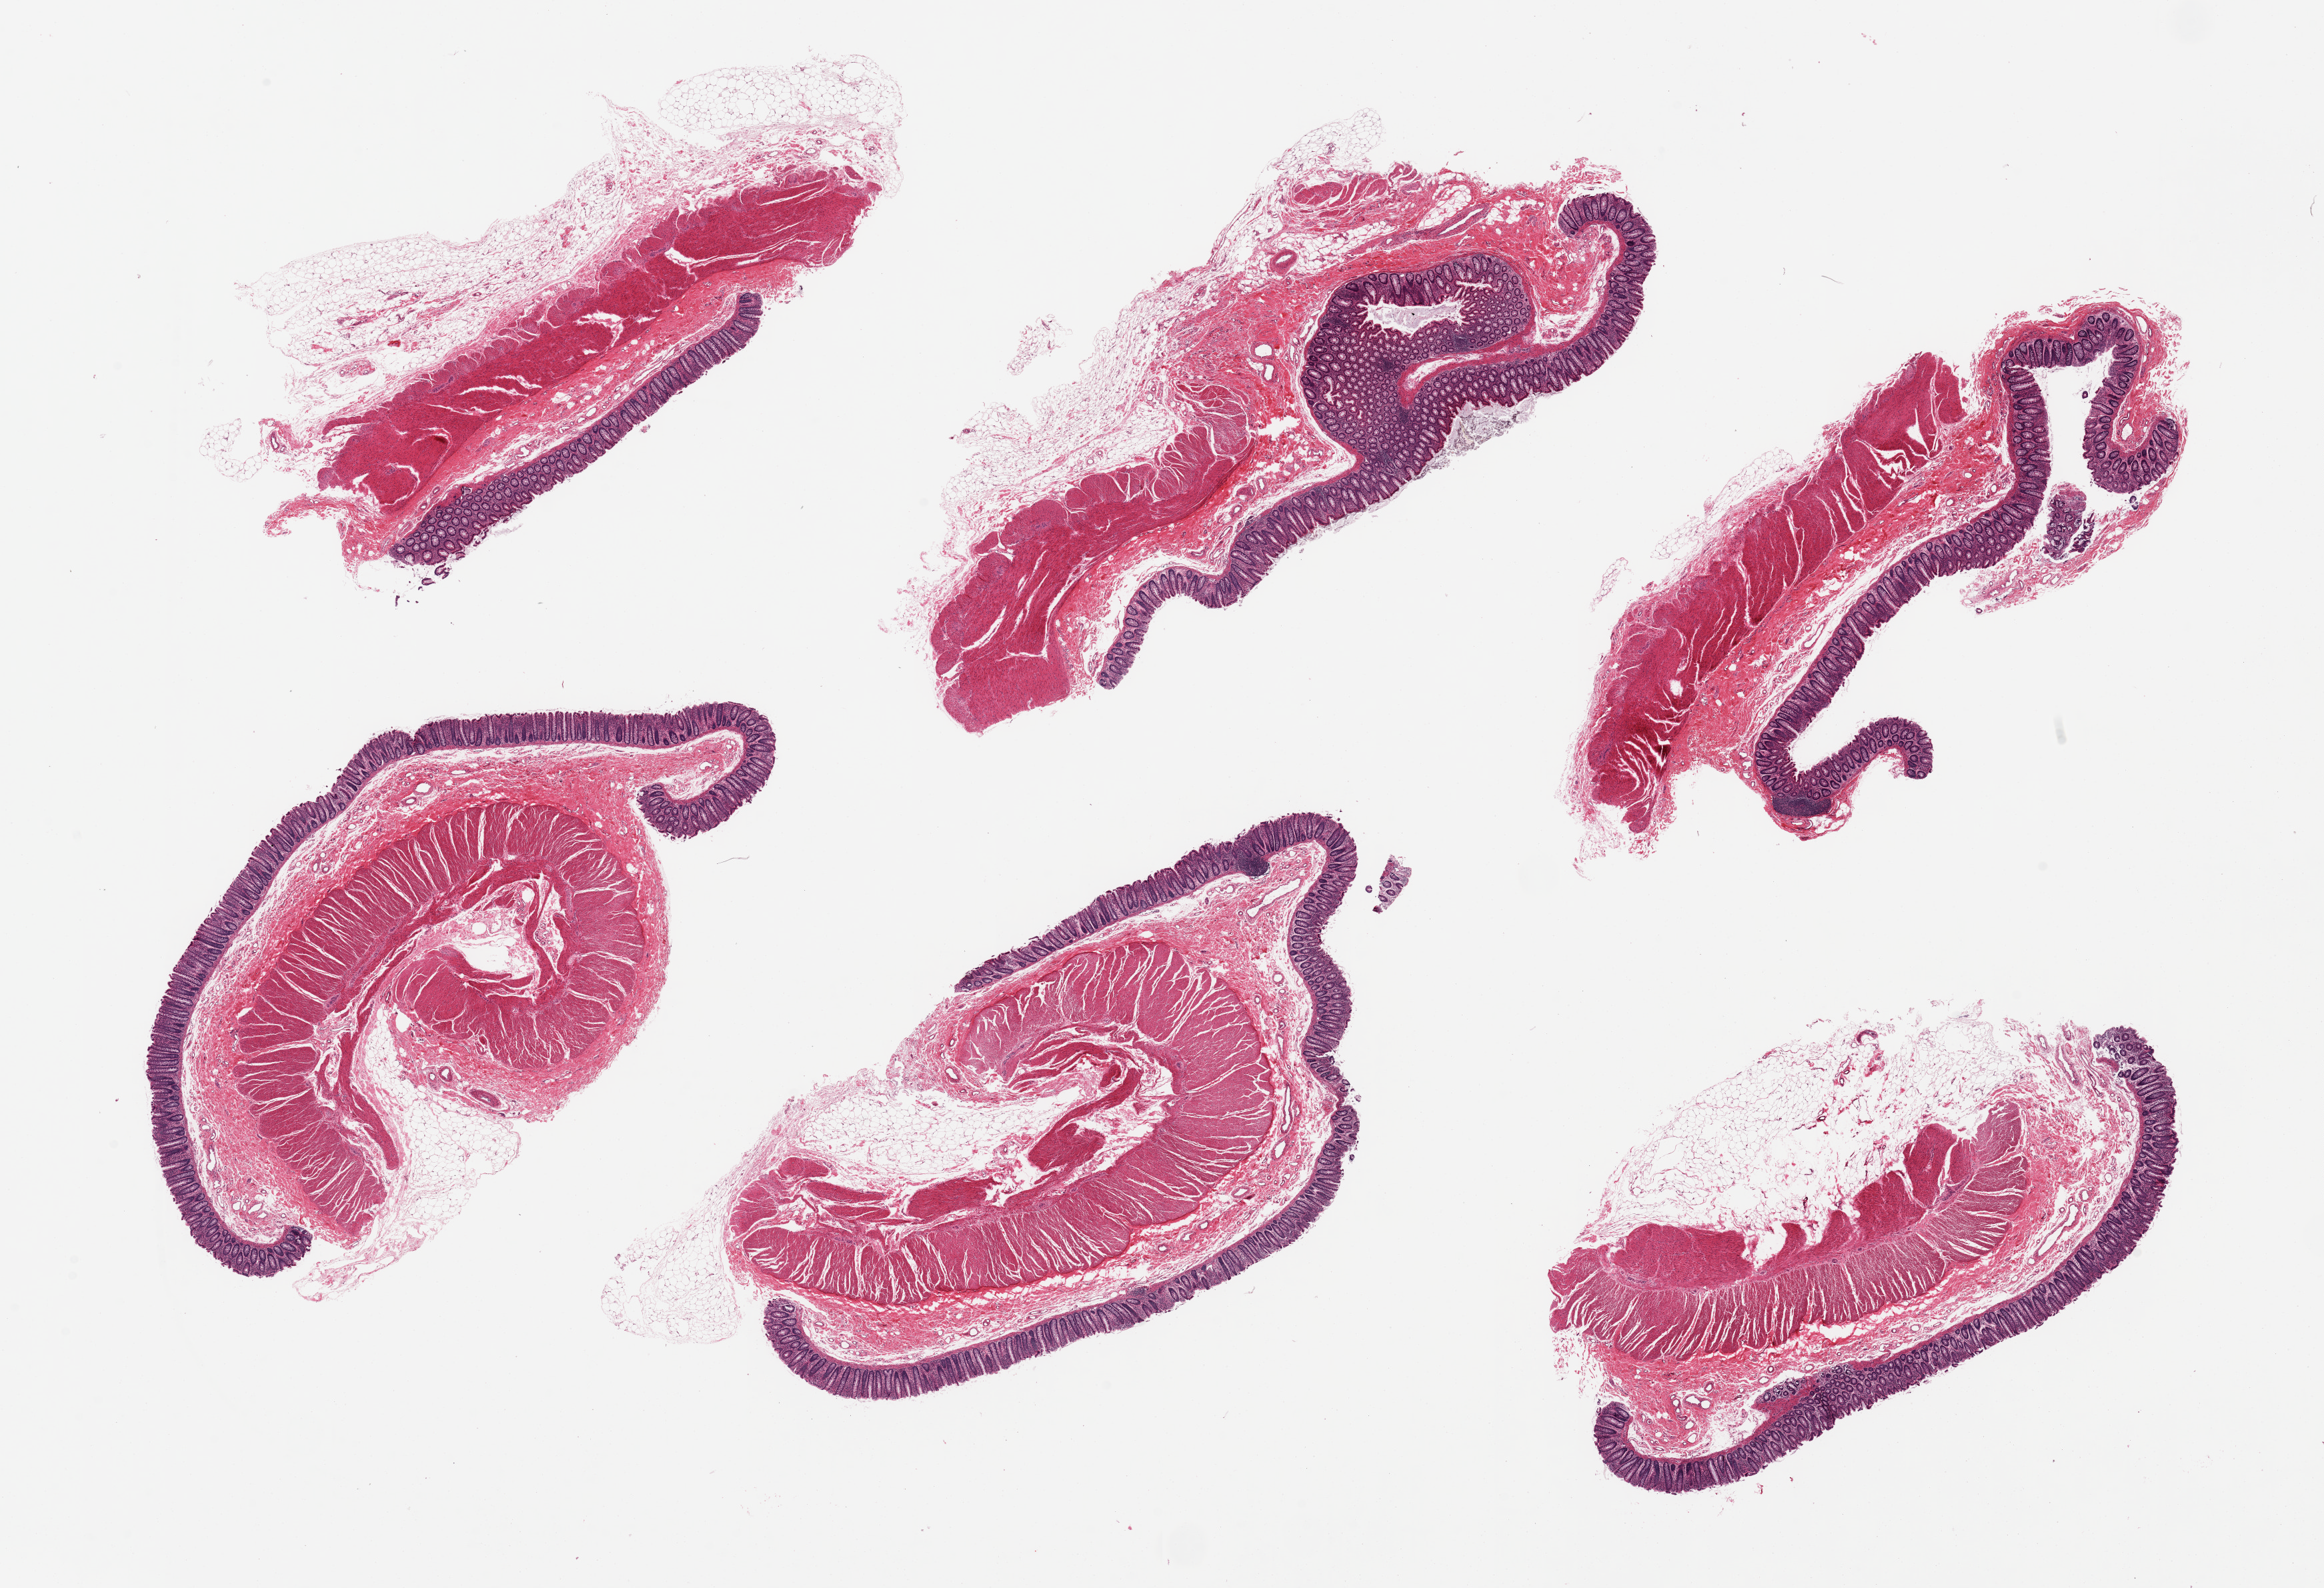
Whole-slide image, haematoxylin and eosin stain, whole scanned area (about 27.6 x 18.8 mm) shown as a low-resolution overview, PAXgene-fixed paraffin-embedded (PFPE) section, target tissue: transverse colon, donor tissue sample. Male donor.
Reviewer comment on this tissue sample: 6 pieces, several with attached adipose tissue from 5-50%.